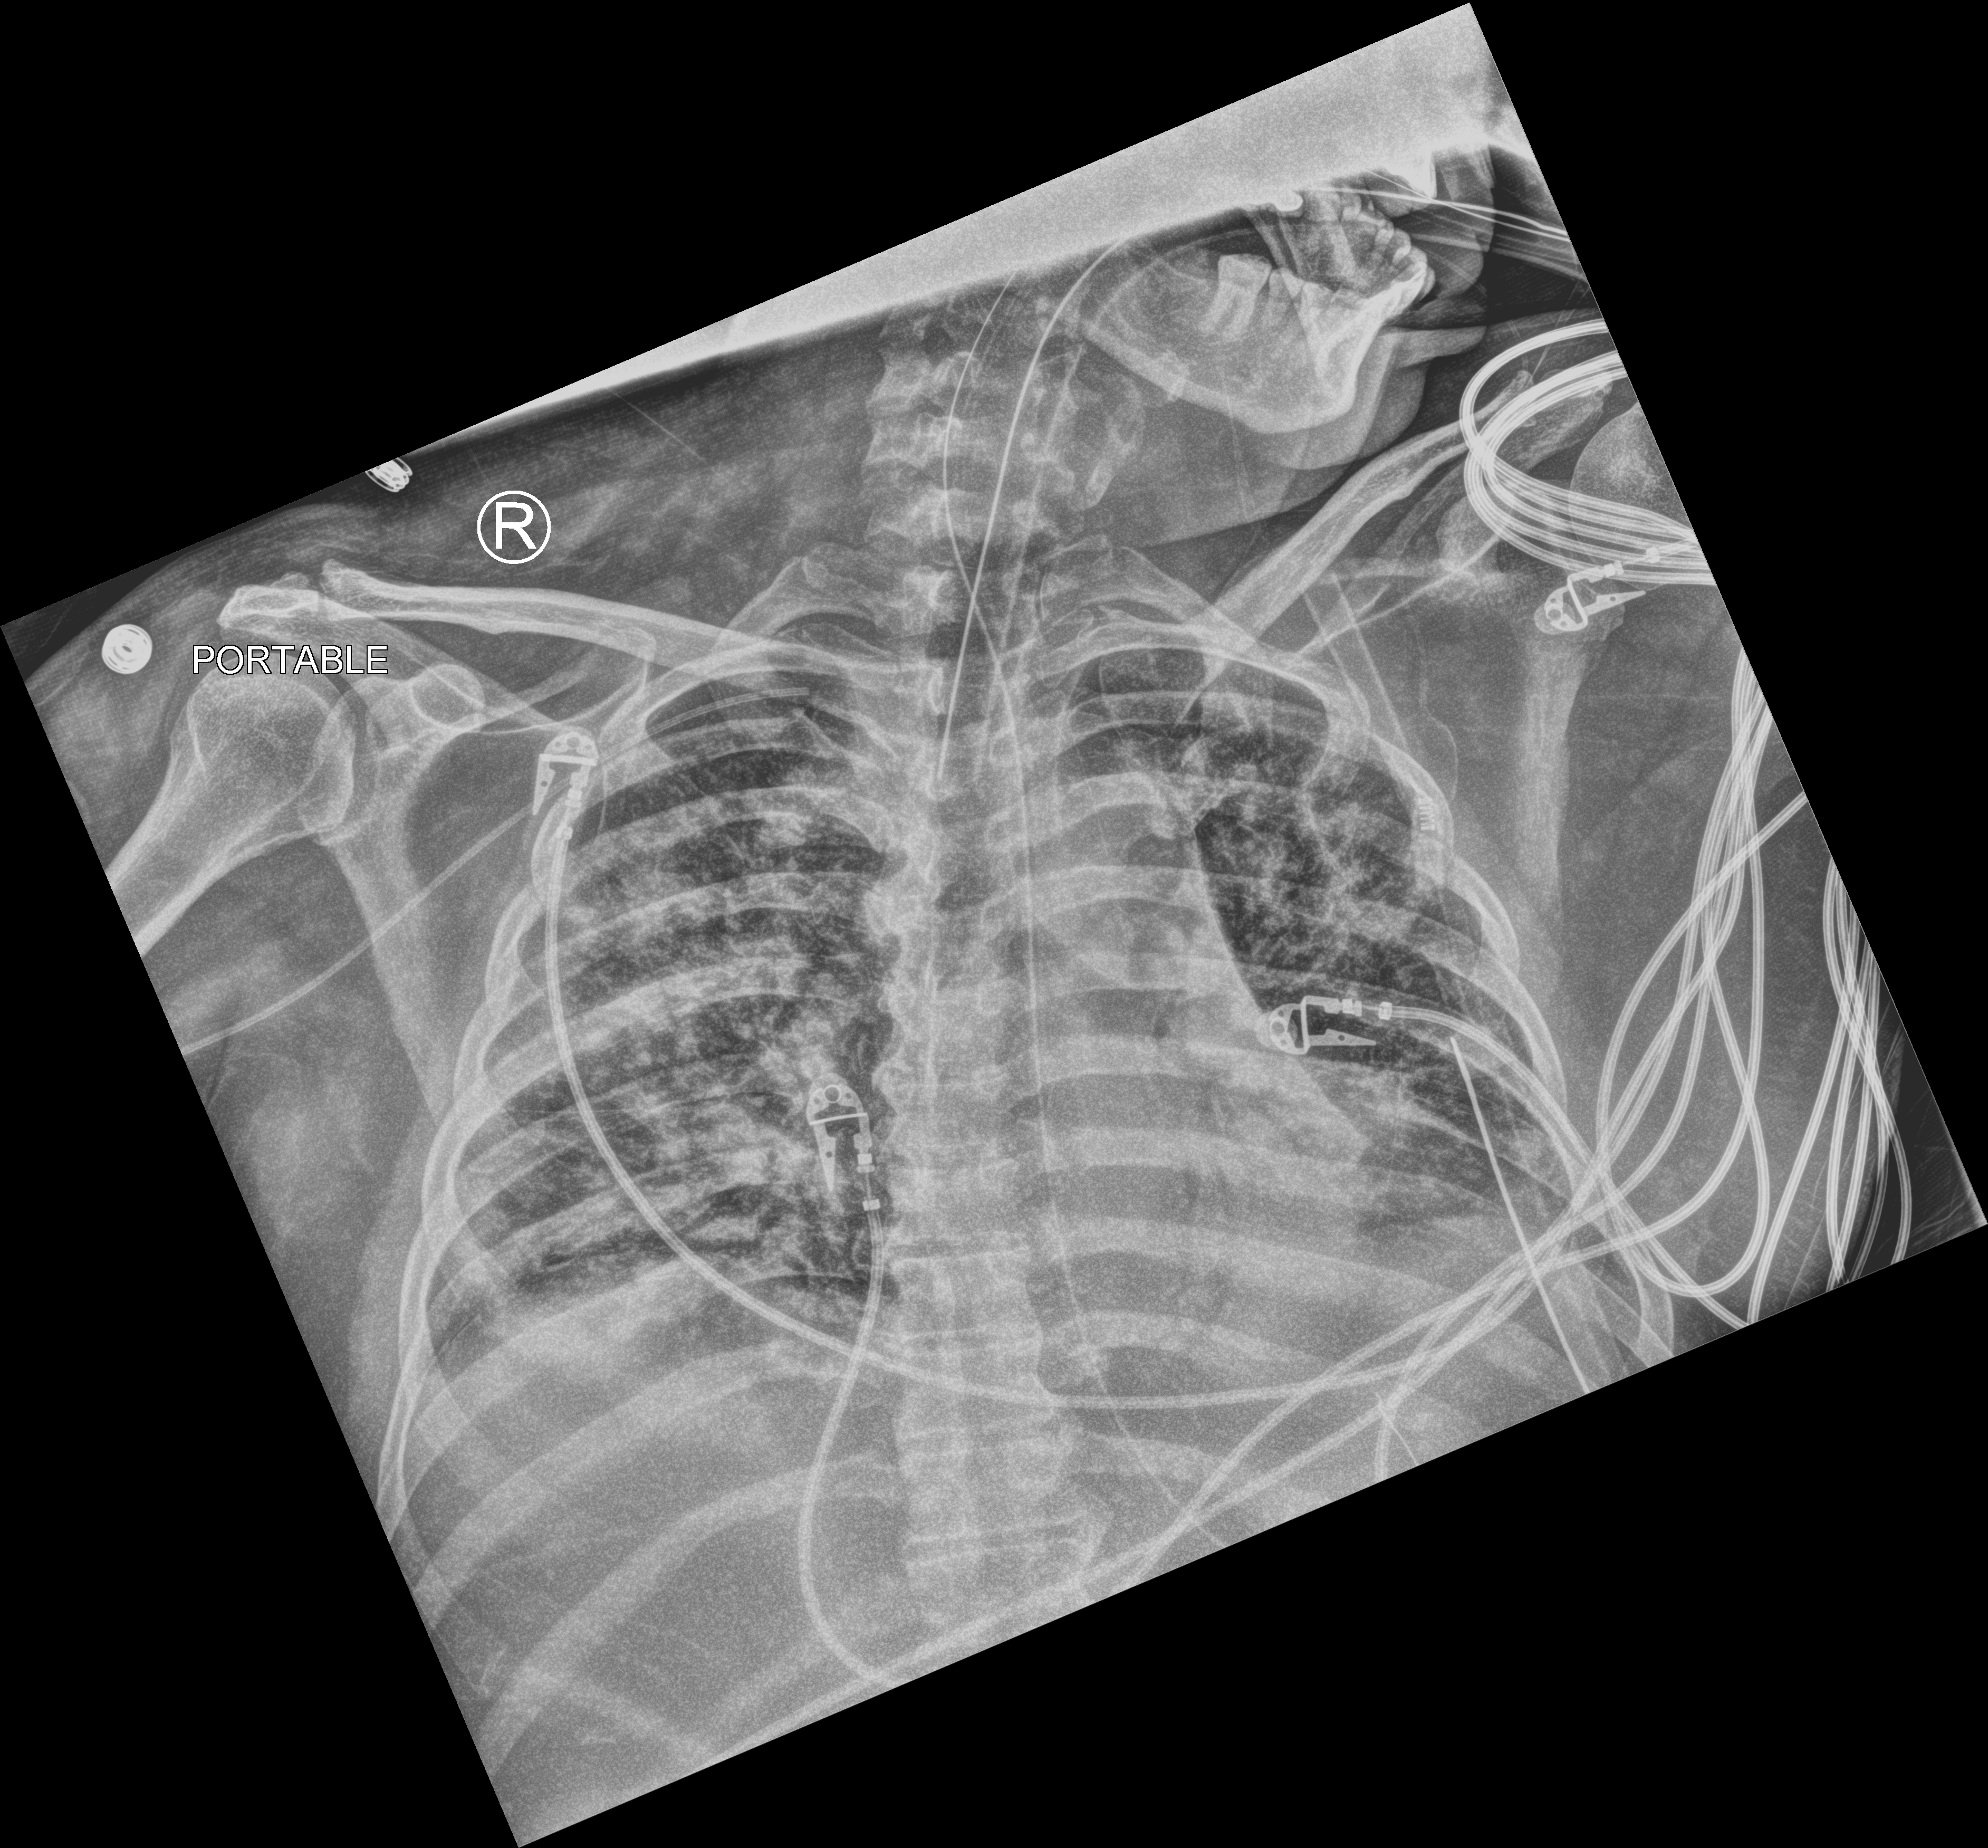
Portable chest radiograph; anteroposterior (AP) projection. Patient hospitalised with COVID-19; male, aged 18–59 years.
Hospital-stay facts (about this admission, not read from this image; timing relative to this image not recorded): admitted to intensive care during this hospital stay: yes; diabetes (admission record): yes.